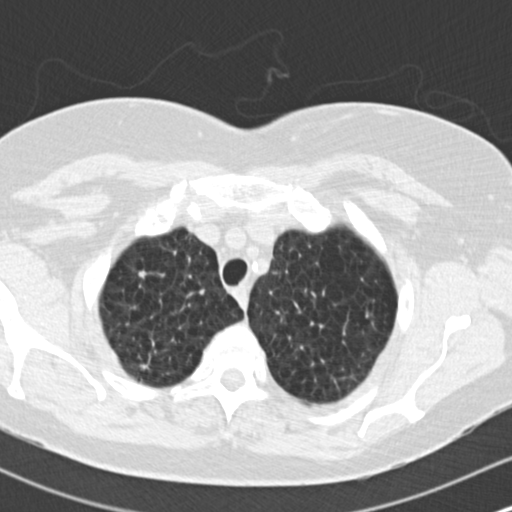
Low-dose screening chest CT, axial slice, first (baseline) screen, lung window (W 1500 / L -600 HU), standard (soft-tissue) reconstruction kernel (B30f), slice 25 of 172 in the series. Female, age 73 years at enrolment. Former smoker at enrolment.
Expert reader's lesion annotation, bounding box [x1, y1, x2, y2] px = [125, 252, 173, 291]. The screening reader recorded 2 non-calcified nodules or masses ≥4 mm on this exam (right upper lobe, right upper lobe); which of them this box marks is not recorded. Later outcome: lung cancer diagnosed 601 days after this screen — adenocarcinoma, NOS, right upper lobe, moderately differentiated (G2), stage IB (AJCC 6th edition), 15 mm at pathology.